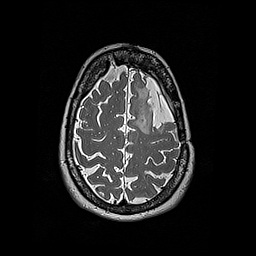
Brain MRI from a brain-tumour surgery series, one axial slice. Slice 141 of 192 in the series (ordered by position). 1 mm slice thickness. 256 × 256 image matrix. From the clinical record (not read from this slice): histopathology: Oligodendroglioma; WHO grade: 2.
Annotated regions visible in this slice (manually delineated by an expert):
- tumour: box from (x=144, y=113) to (x=154, y=133) px